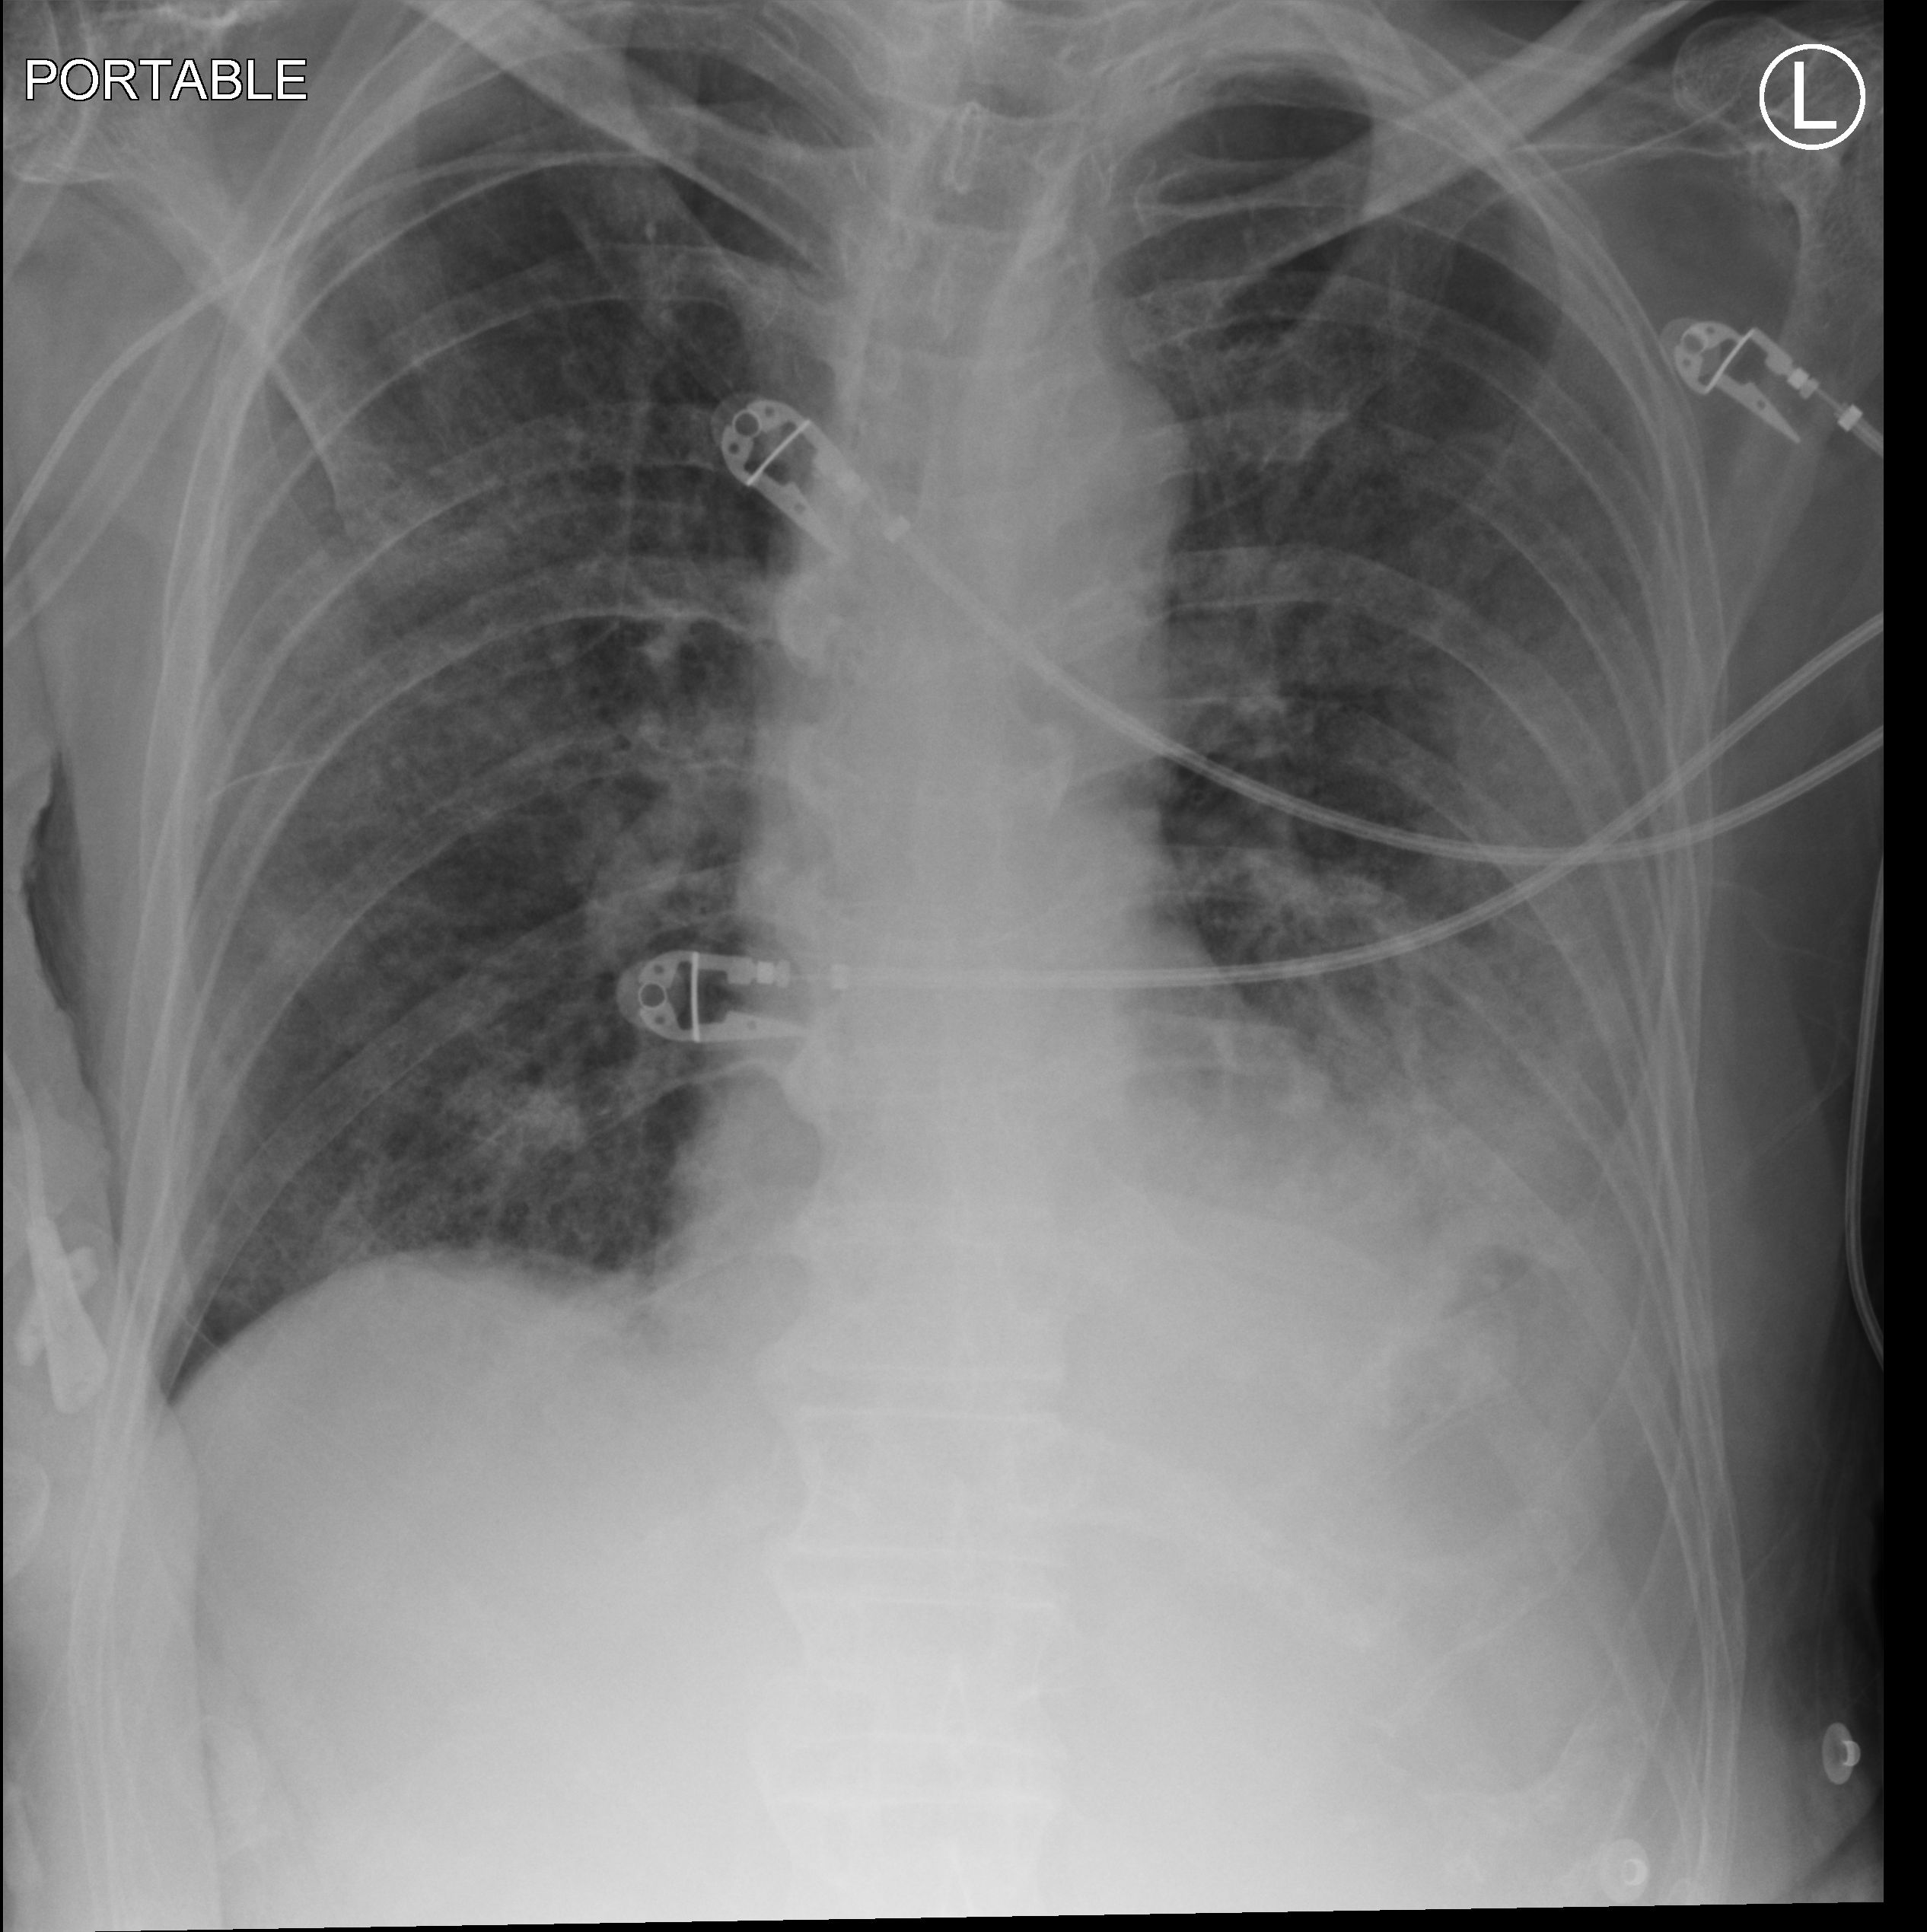
Bedside chest radiograph (computed radiography). Patient hospitalised with COVID-19; male, aged 60–74 years.
Hospital-stay facts (about this admission, not read from this image; timing relative to this image not recorded):
- other chronic lung disease (admission record): no
- admitted to intensive care during this hospital stay: yes